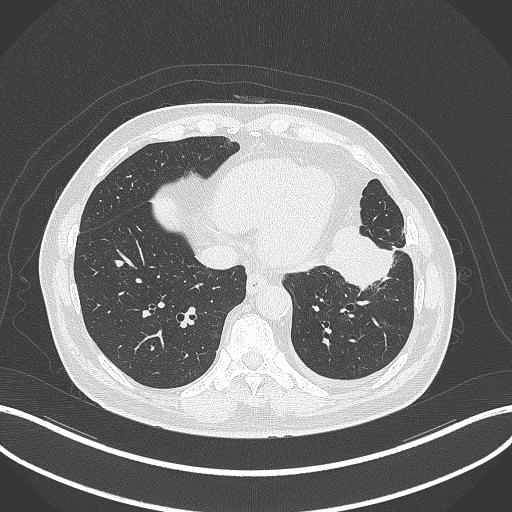
Chest CT, one axial slice; slice 104 of 230 in the series (ordered by position); 120 kVp; lung window (W 1500 / L -600 HU); 1 mm slice thickness; 512 × 512 image matrix. Patient: male, 68 years. From the clinical record (not read from this slice): clinical TNM (as recorded): T2b N0 M0.
Structures marked on this image (bounding box drawn by a radiologist):
- lung tumour (recorded histology: squamous cell carcinoma): box from (x=325, y=222) to (x=396, y=294) px